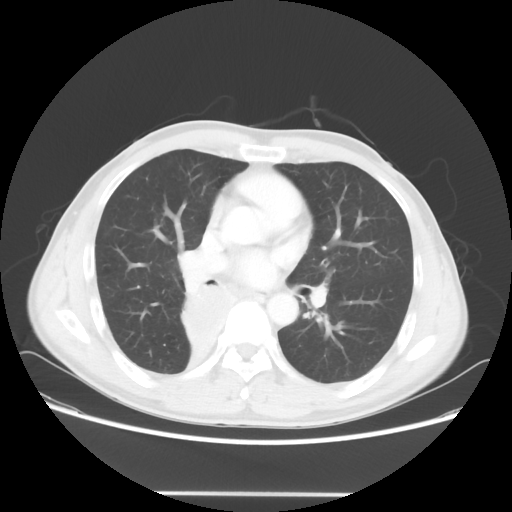
Chest CT, one axial slice; slice 33 of 62 in the series (ordered by position); reconstruction kernel STANDARD; lung window (W 1500 / L -600 HU); 5 mm slice thickness; 512 × 512 image matrix, field of view 393 × 393 mm. Patient: male, 47 years. From the clinical record (not read from this slice): clinical TNM (as recorded): T2 N0 M0; histopathological grade: G2.
Outlined on this slice (bounding box drawn by a radiologist):
- lung tumour (recorded histology: squamous cell carcinoma): bounding box [x1, y1, x2, y2] px = [177, 277, 246, 356]